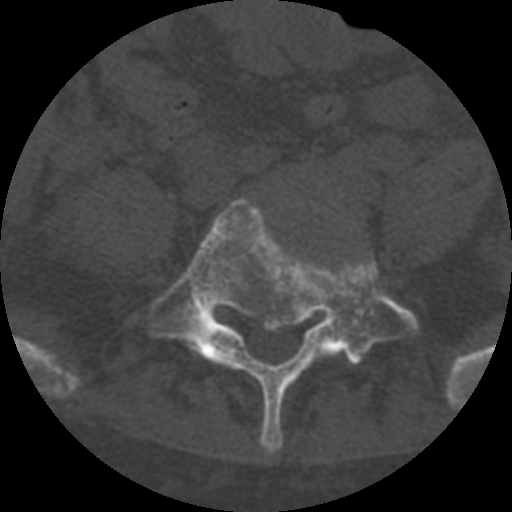
CT including the spine, one axial slice. Slice 187 of 708 in the series (ordered by position). Reconstruction kernel STANDARD. One of 3 acquisitions stored at this slice position. Bone window (W 1800 / L 400 HU). 1.25 mm slice thickness. 512 × 512 image matrix, field of view 160 × 160 mm. Patient age 55 years. Case-level facts recorded for this patient, not image findings: primary cancer: colon; vertebrae with lytic lesions (as recorded): T12, L1, L5.
Structures marked on this image (semi-automatically segmented with operator editing):
- L5 vertebra: bounding box (x1, y1, x2, y2) in pixels: (129, 189, 420, 453)